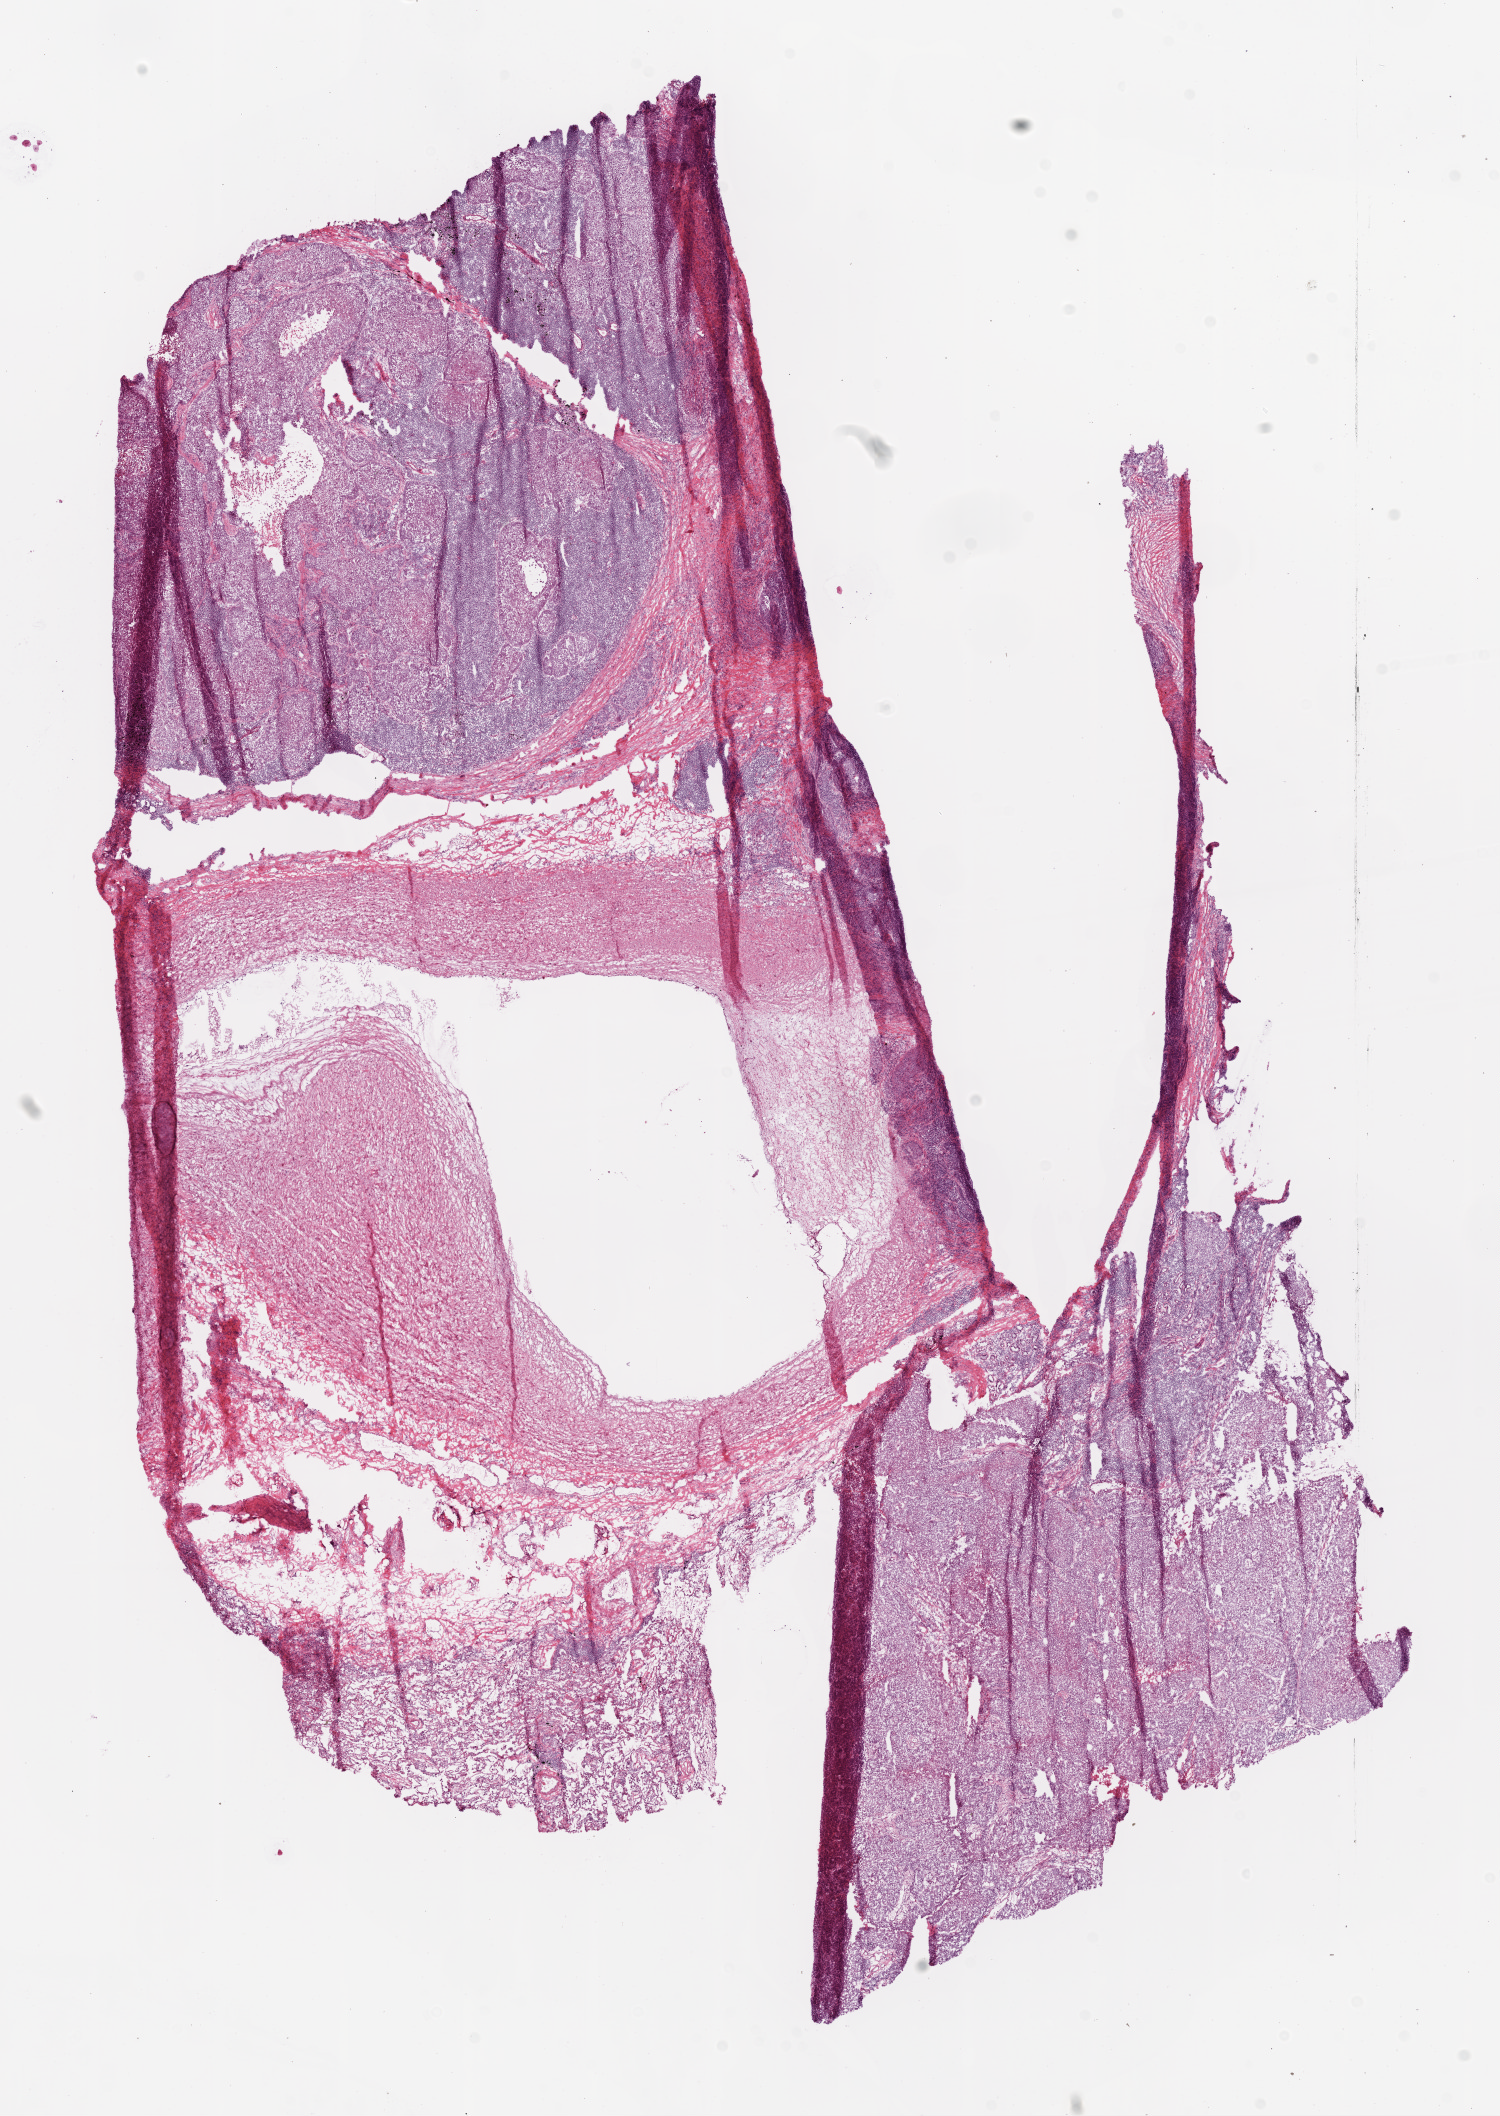
Whole-slide histology image, H&E, a low-resolution overview of the entire scanned area, about 12.0 x 17.0 mm (acquisition: 20x scan). Frozen section from the bottom of the tissue portion. Primary tumour sample from the lung. Patient: male, age at initial diagnosis 70 years. Slide review estimates, as recorded: tumour cells 85%, tumour nuclei 90%, normal cells 0%, stromal cells 15%, necrosis 5%.
- AJCC pathologic stage: IIB
- diagnosis: Squamous cell carcinoma, NOS